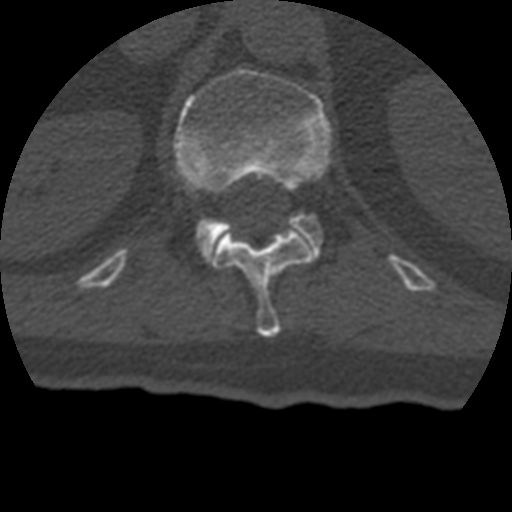
CT including the spine, one axial slice. Slice 160 of 399 in the series (ordered by position). 120 kVp. Bone window (W 1800 / L 400 HU). 512 × 512 image matrix, field of view 160 × 160 mm. Patient age 69 years. Case-level facts recorded for this patient, not image findings: primary cancer: prostate.
Annotated regions visible in this slice (semi-automatic segmentation, software-assisted and operator-edited):
- L1 vertebra: bounding box [x1, y1, x2, y2] px = [173, 68, 332, 263]
- T12 vertebra: [214, 229, 315, 337]